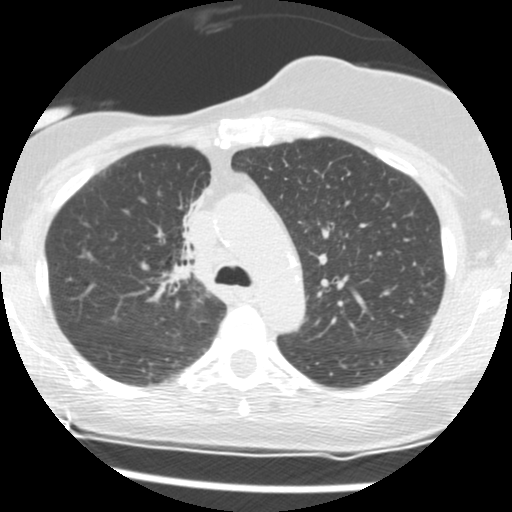
Low-dose screening chest CT, axial slice; second annual screen; lung window (W 1500 / L -600 HU); 2.5 mm slice thickness; standard (soft-tissue) reconstruction kernel (STANDARD); slice 42 of 165 in the series; 512 × 512 image matrix. Female participant, aged 56 years at enrolment.
Lesion marked by an expert reader, bounding box (x1, y1, x2, y2) in pixels: (154, 190, 212, 272). The screening reader recorded 2 non-calcified nodules or masses ≥4 mm on this exam (right middle lobe, right lower lobe); which of them this box marks is not recorded.